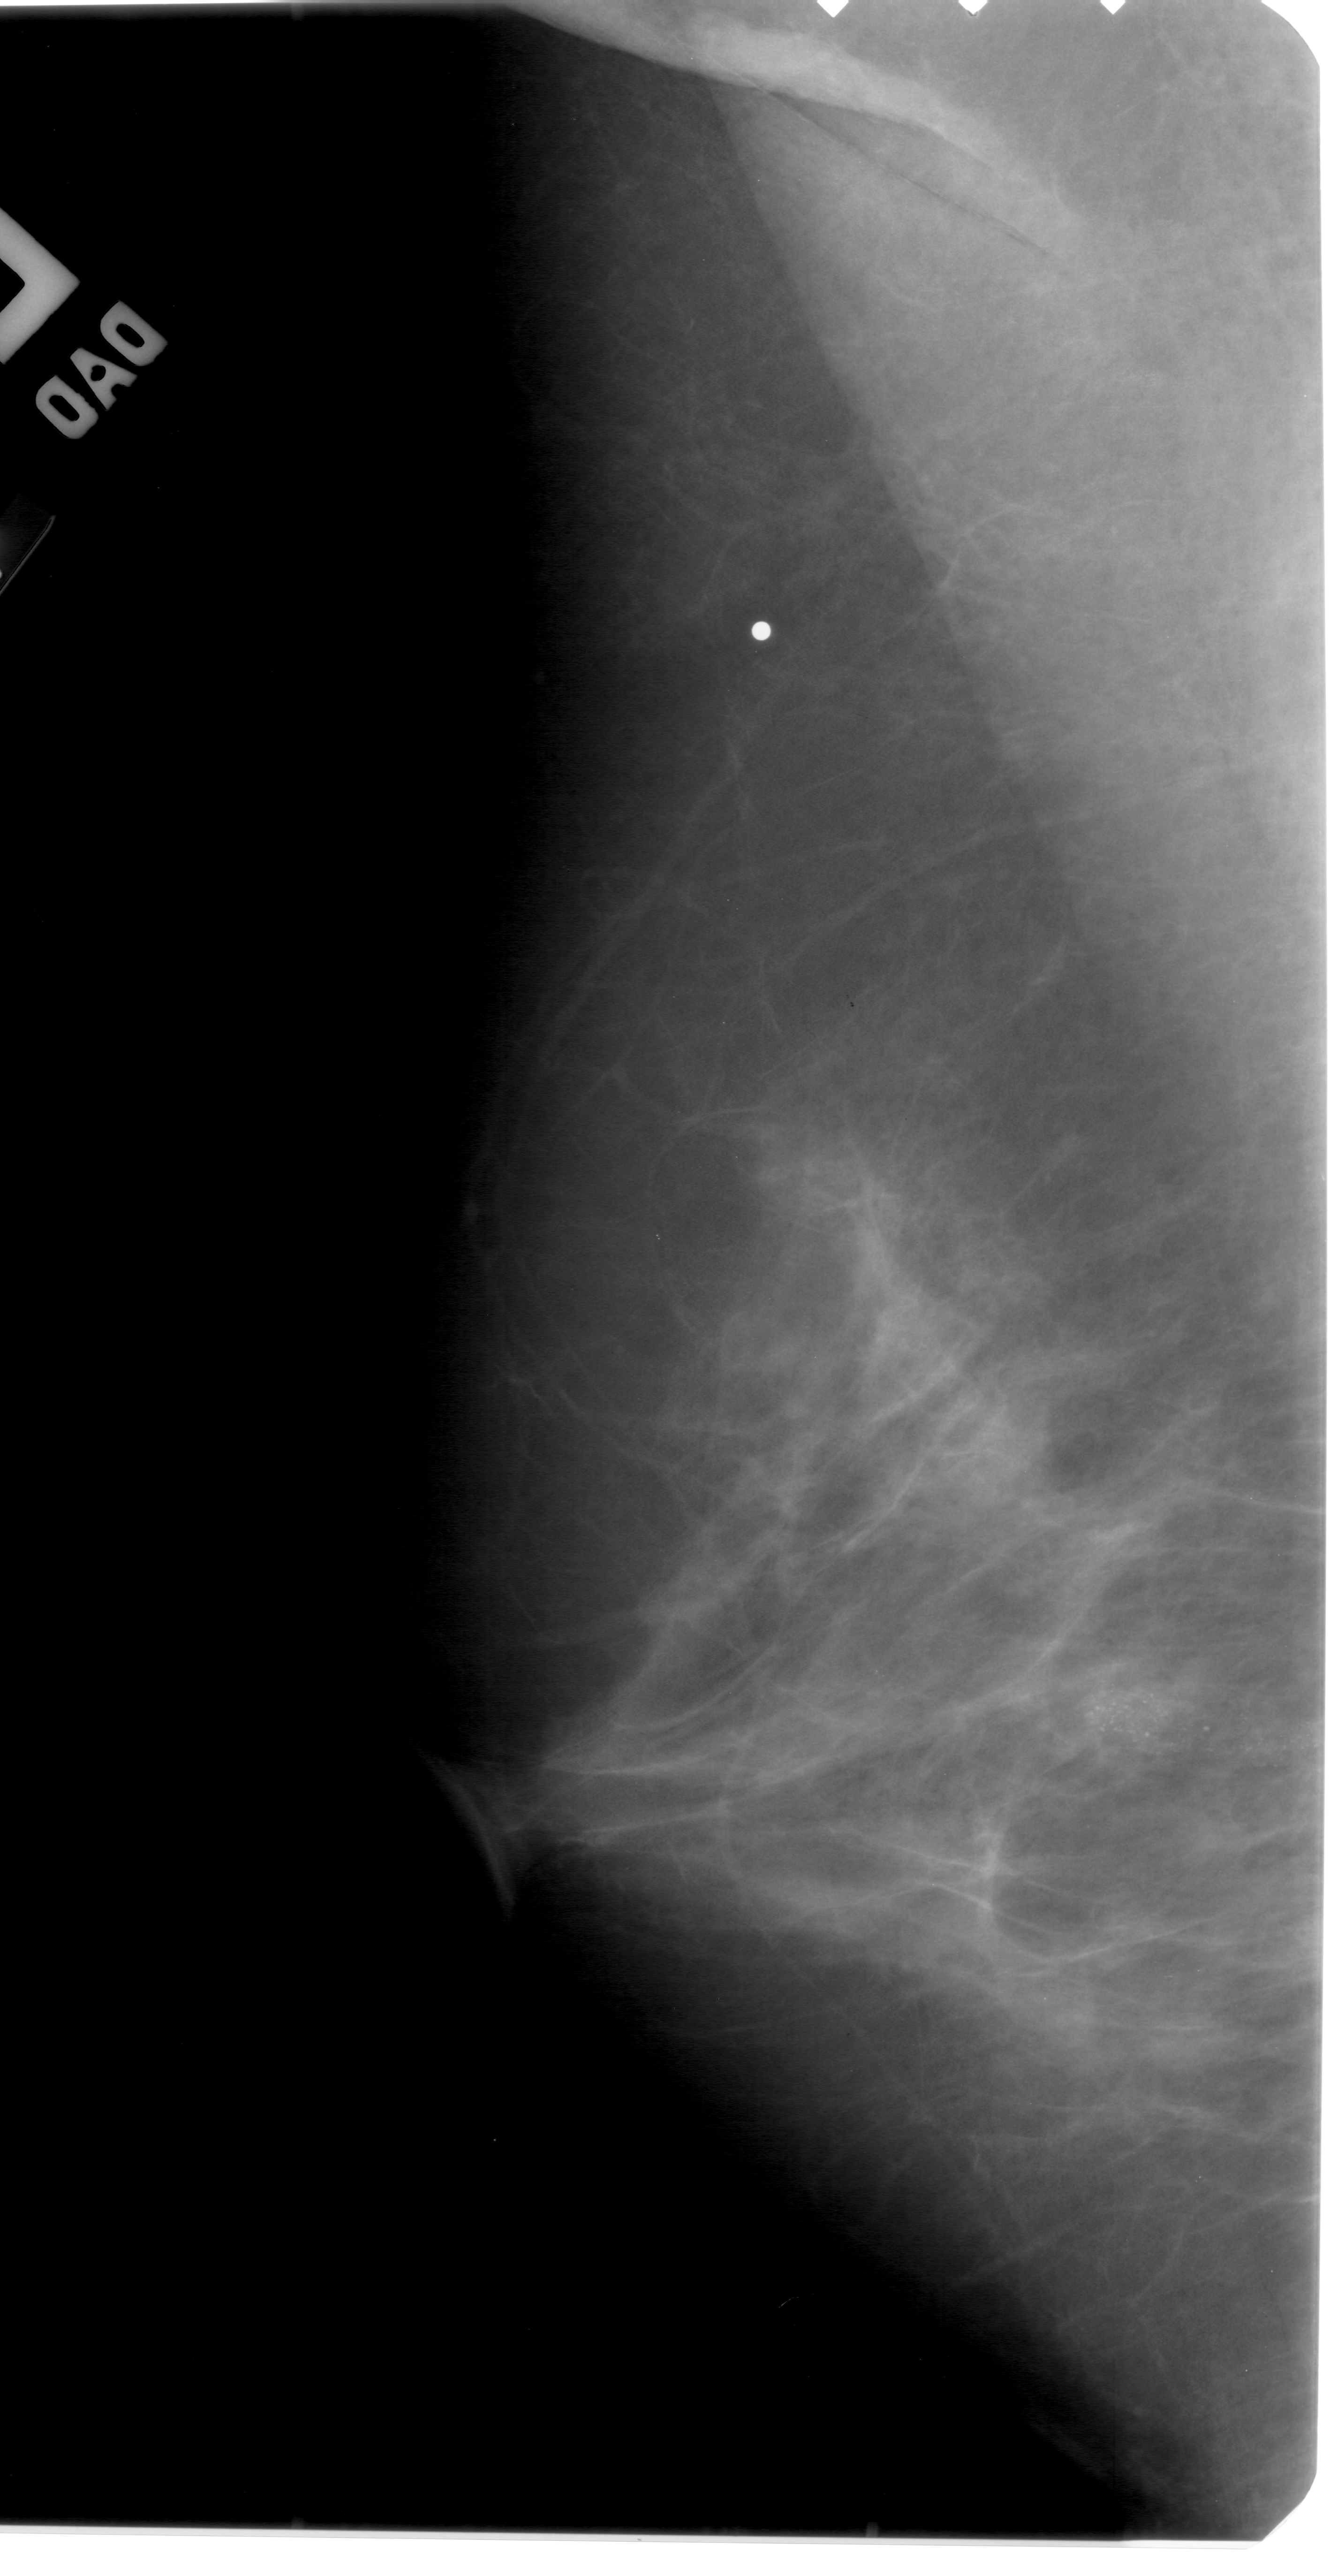
Scanned film-screen mammogram. Left breast. Mediolateral oblique (MLO) view. BI-RADS breast density category 1 (scale 1–4). 1337 × 2576 image matrix.
Expert-marked regions of interest on this film, with their recorded descriptors:
- calcifications, morphology pleomorphic, distribution clustered; BI-RADS assessment category 4; subtlety rating 3 on a 1 (subtle) to 5 (obvious) scale; pathology (as recorded): benign: box from (x=1065, y=1675) to (x=1322, y=1801) px